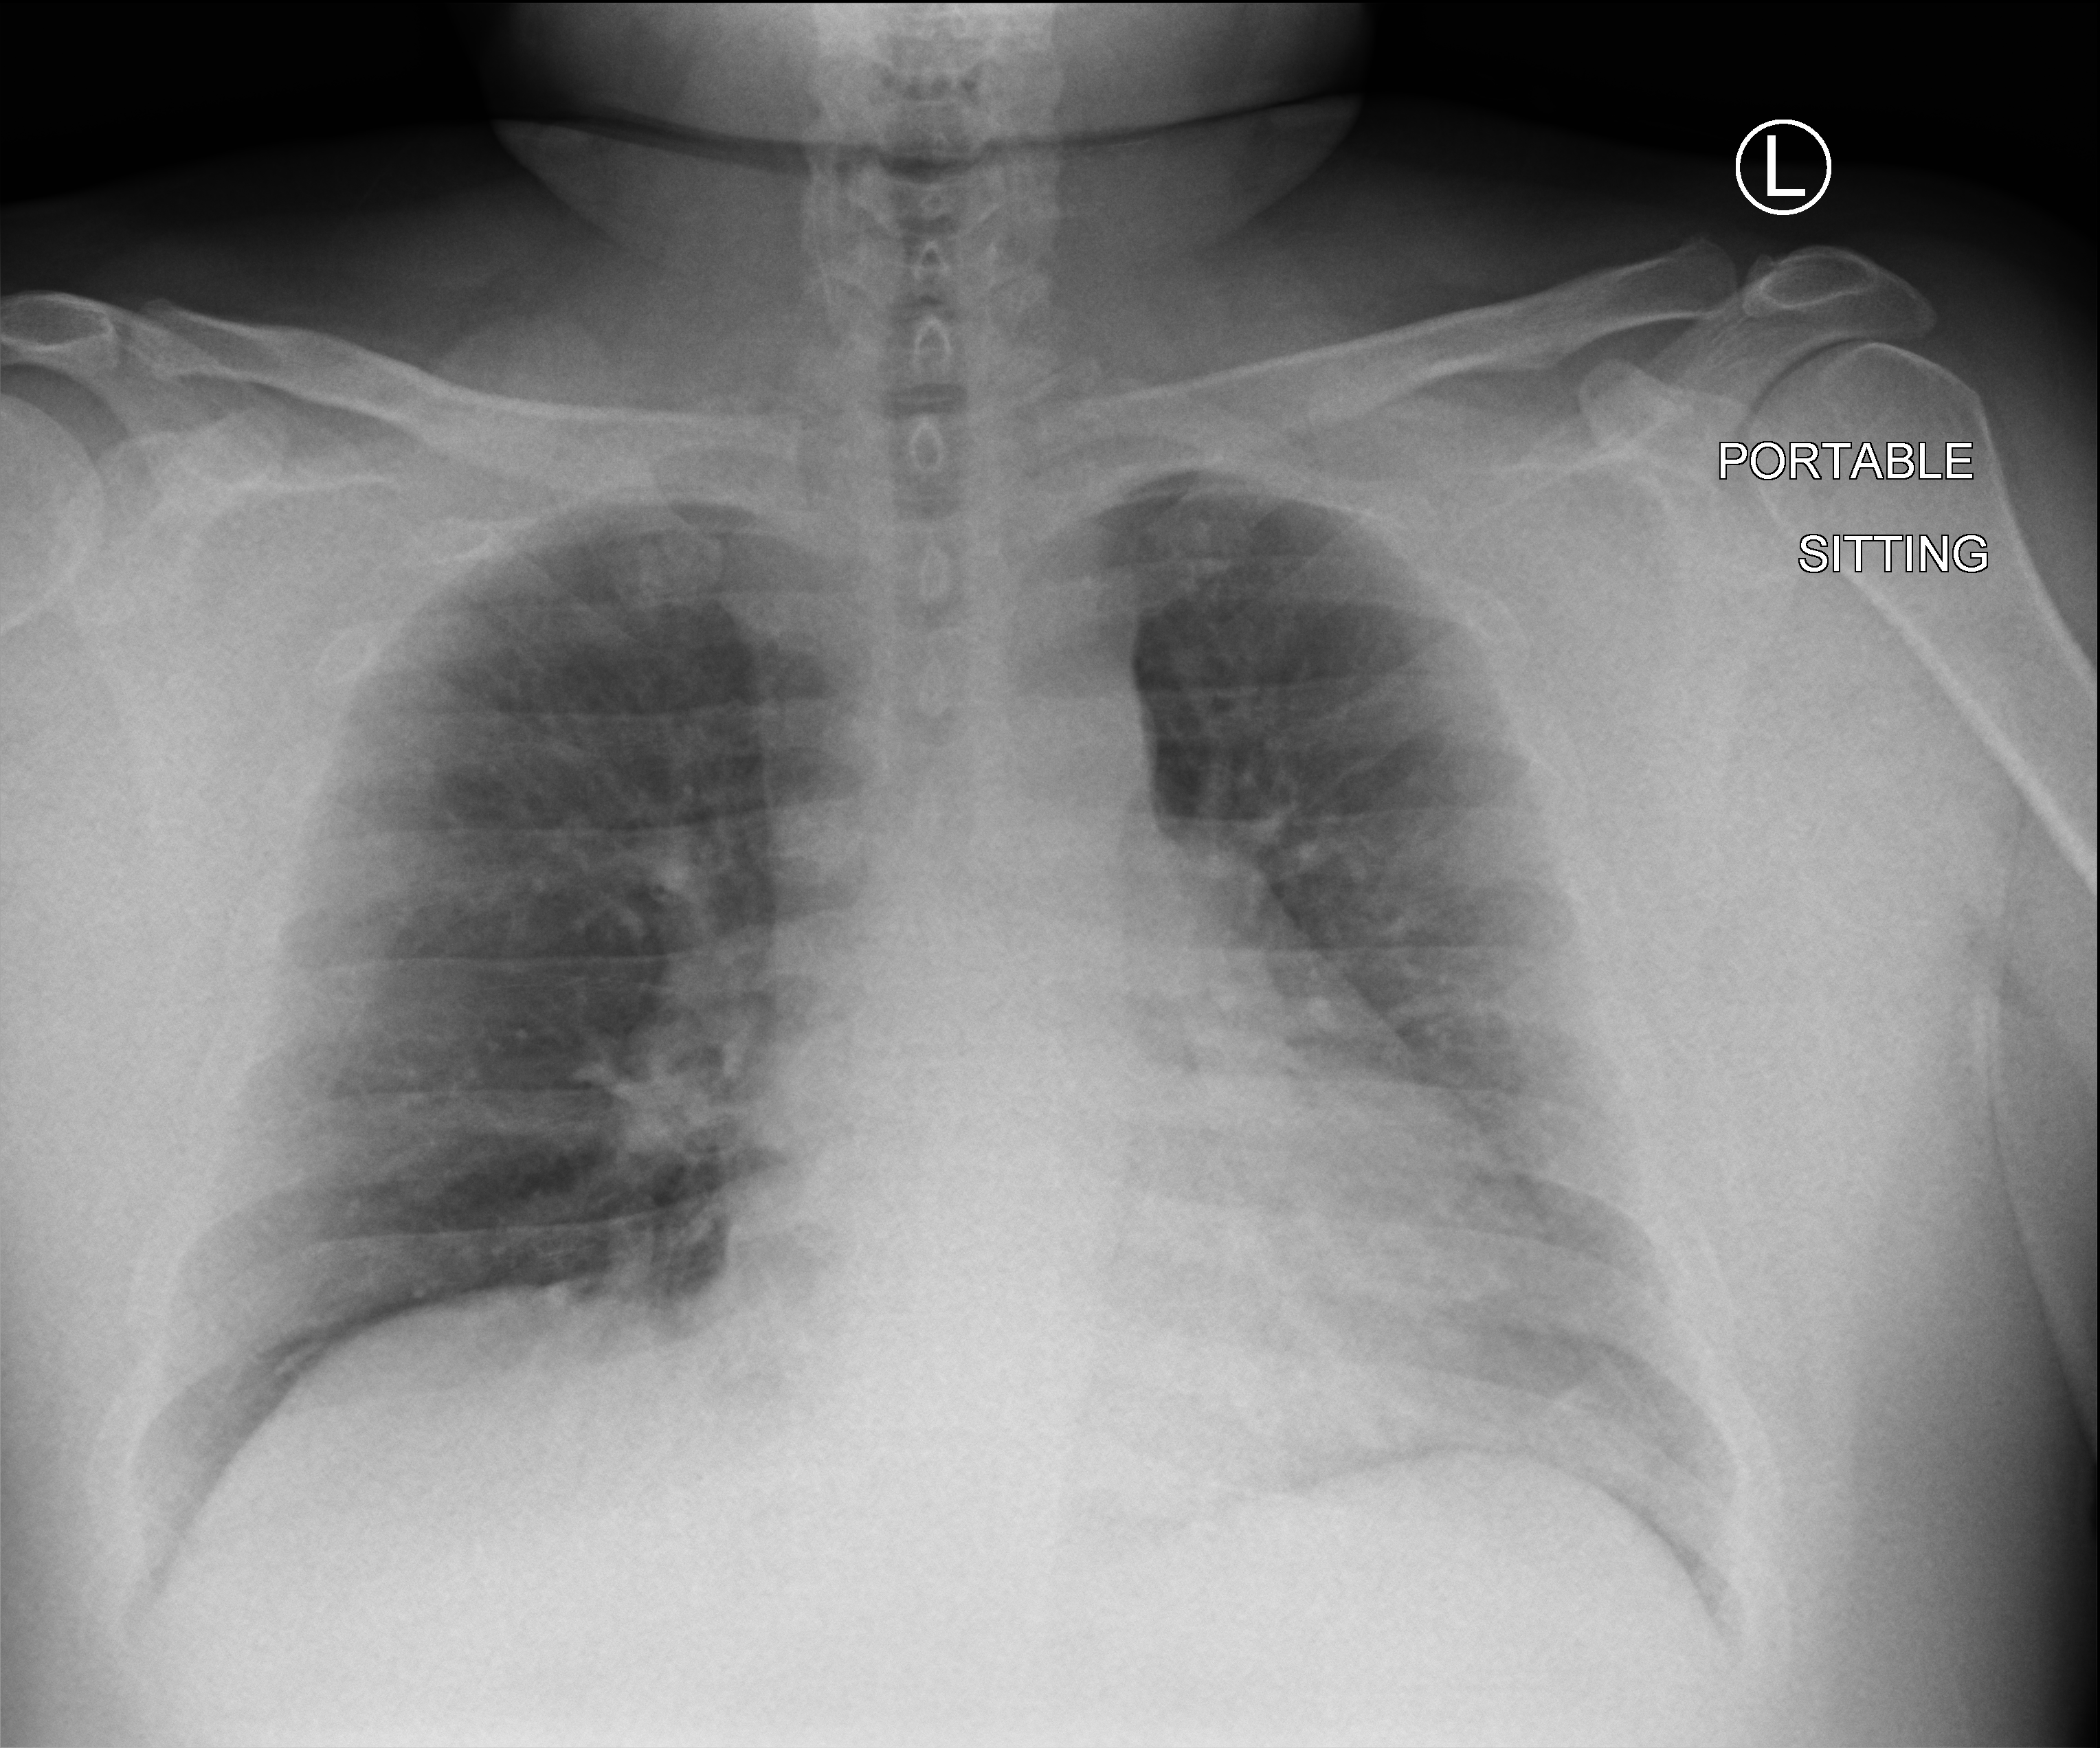
Chest X-ray (portable); anteroposterior (AP) projection. Patient hospitalised with COVID-19, aged 18–59 years.
Hospital-stay facts (about this admission, not read from this image; timing relative to this image not recorded): chronic kidney disease (admission record): no; admitted to intensive care during this hospital stay: yes.